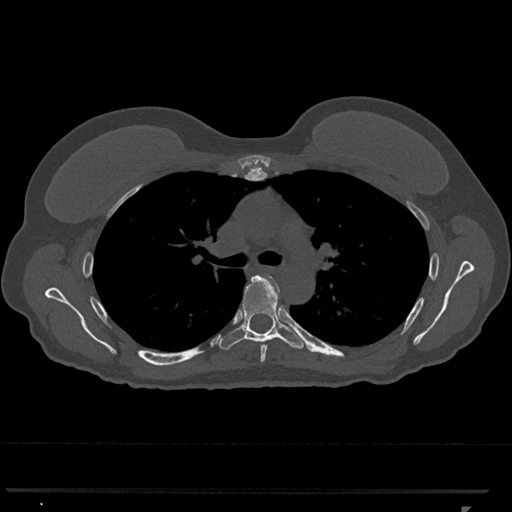
CT including the spine, one axial slice. Position 775 of 793 along the scan axis. Reconstruction kernel Br40s/3. Bone window (W 1800 / L 400 HU). 512 × 512 image matrix. Female patient, age 62 years. Case-level facts recorded for this patient, not image findings: primary cancer: renal.
Structures marked on this image (semi-automatically segmented with operator editing):
- T5 vertebra: bounding box (x1, y1, x2, y2) in pixels: (260, 278, 279, 362)
- T6 vertebra: (219, 274, 304, 350)